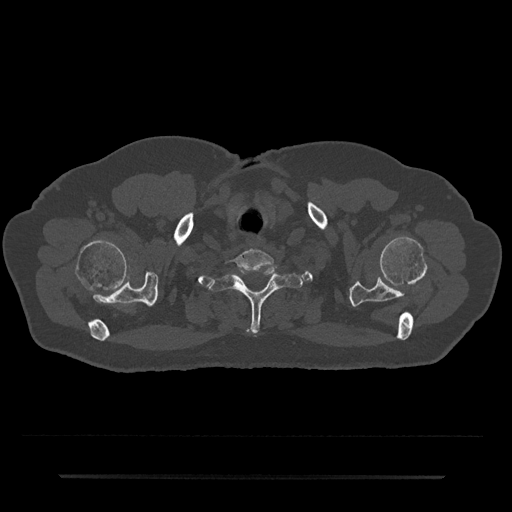
CT including the spine, one axial slice; slice 648 of 797 in the series (ordered by position); reconstruction kernel Br40s/3; 120 kVp; bone window (W 1800 / L 400 HU); 0.5 mm slice thickness; 512 × 512 image matrix, field of view 437 × 437 mm. Male patient, age 69 years. From the clinical record (not read from this slice): primary cancer: prostate.
Structures marked on this image (semi-automatic segmentation, software-assisted and operator-edited):
- T1 vertebra: bounding box (x1, y1, x2, y2) in pixels: (209, 267, 304, 335)